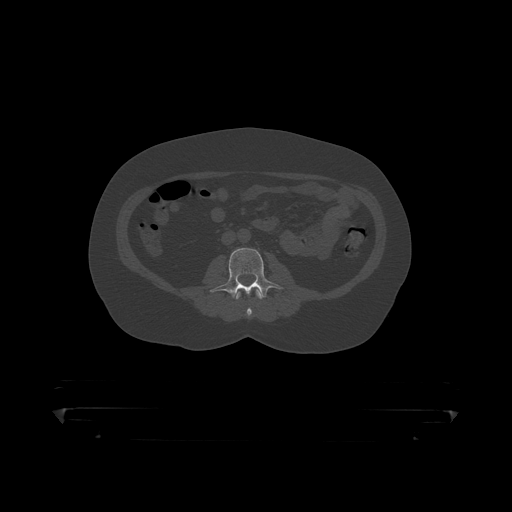
CT including the spine, one axial slice; position 94 of 390 along the scan axis; reconstruction kernel STANDARD; 120 kVp; bone window (W 1800 / L 400 HU); 512 × 512 image matrix. Male patient, age 60 years. Case-level facts recorded for this patient, not image findings: primary cancer: prostate.
Outlined on this slice (semi-automatic segmentation, software-assisted and operator-edited):
- L2 vertebra: bounding box (x1, y1, x2, y2) in pixels: (236, 289, 264, 319)
- L3 vertebra: (209, 249, 282, 300)